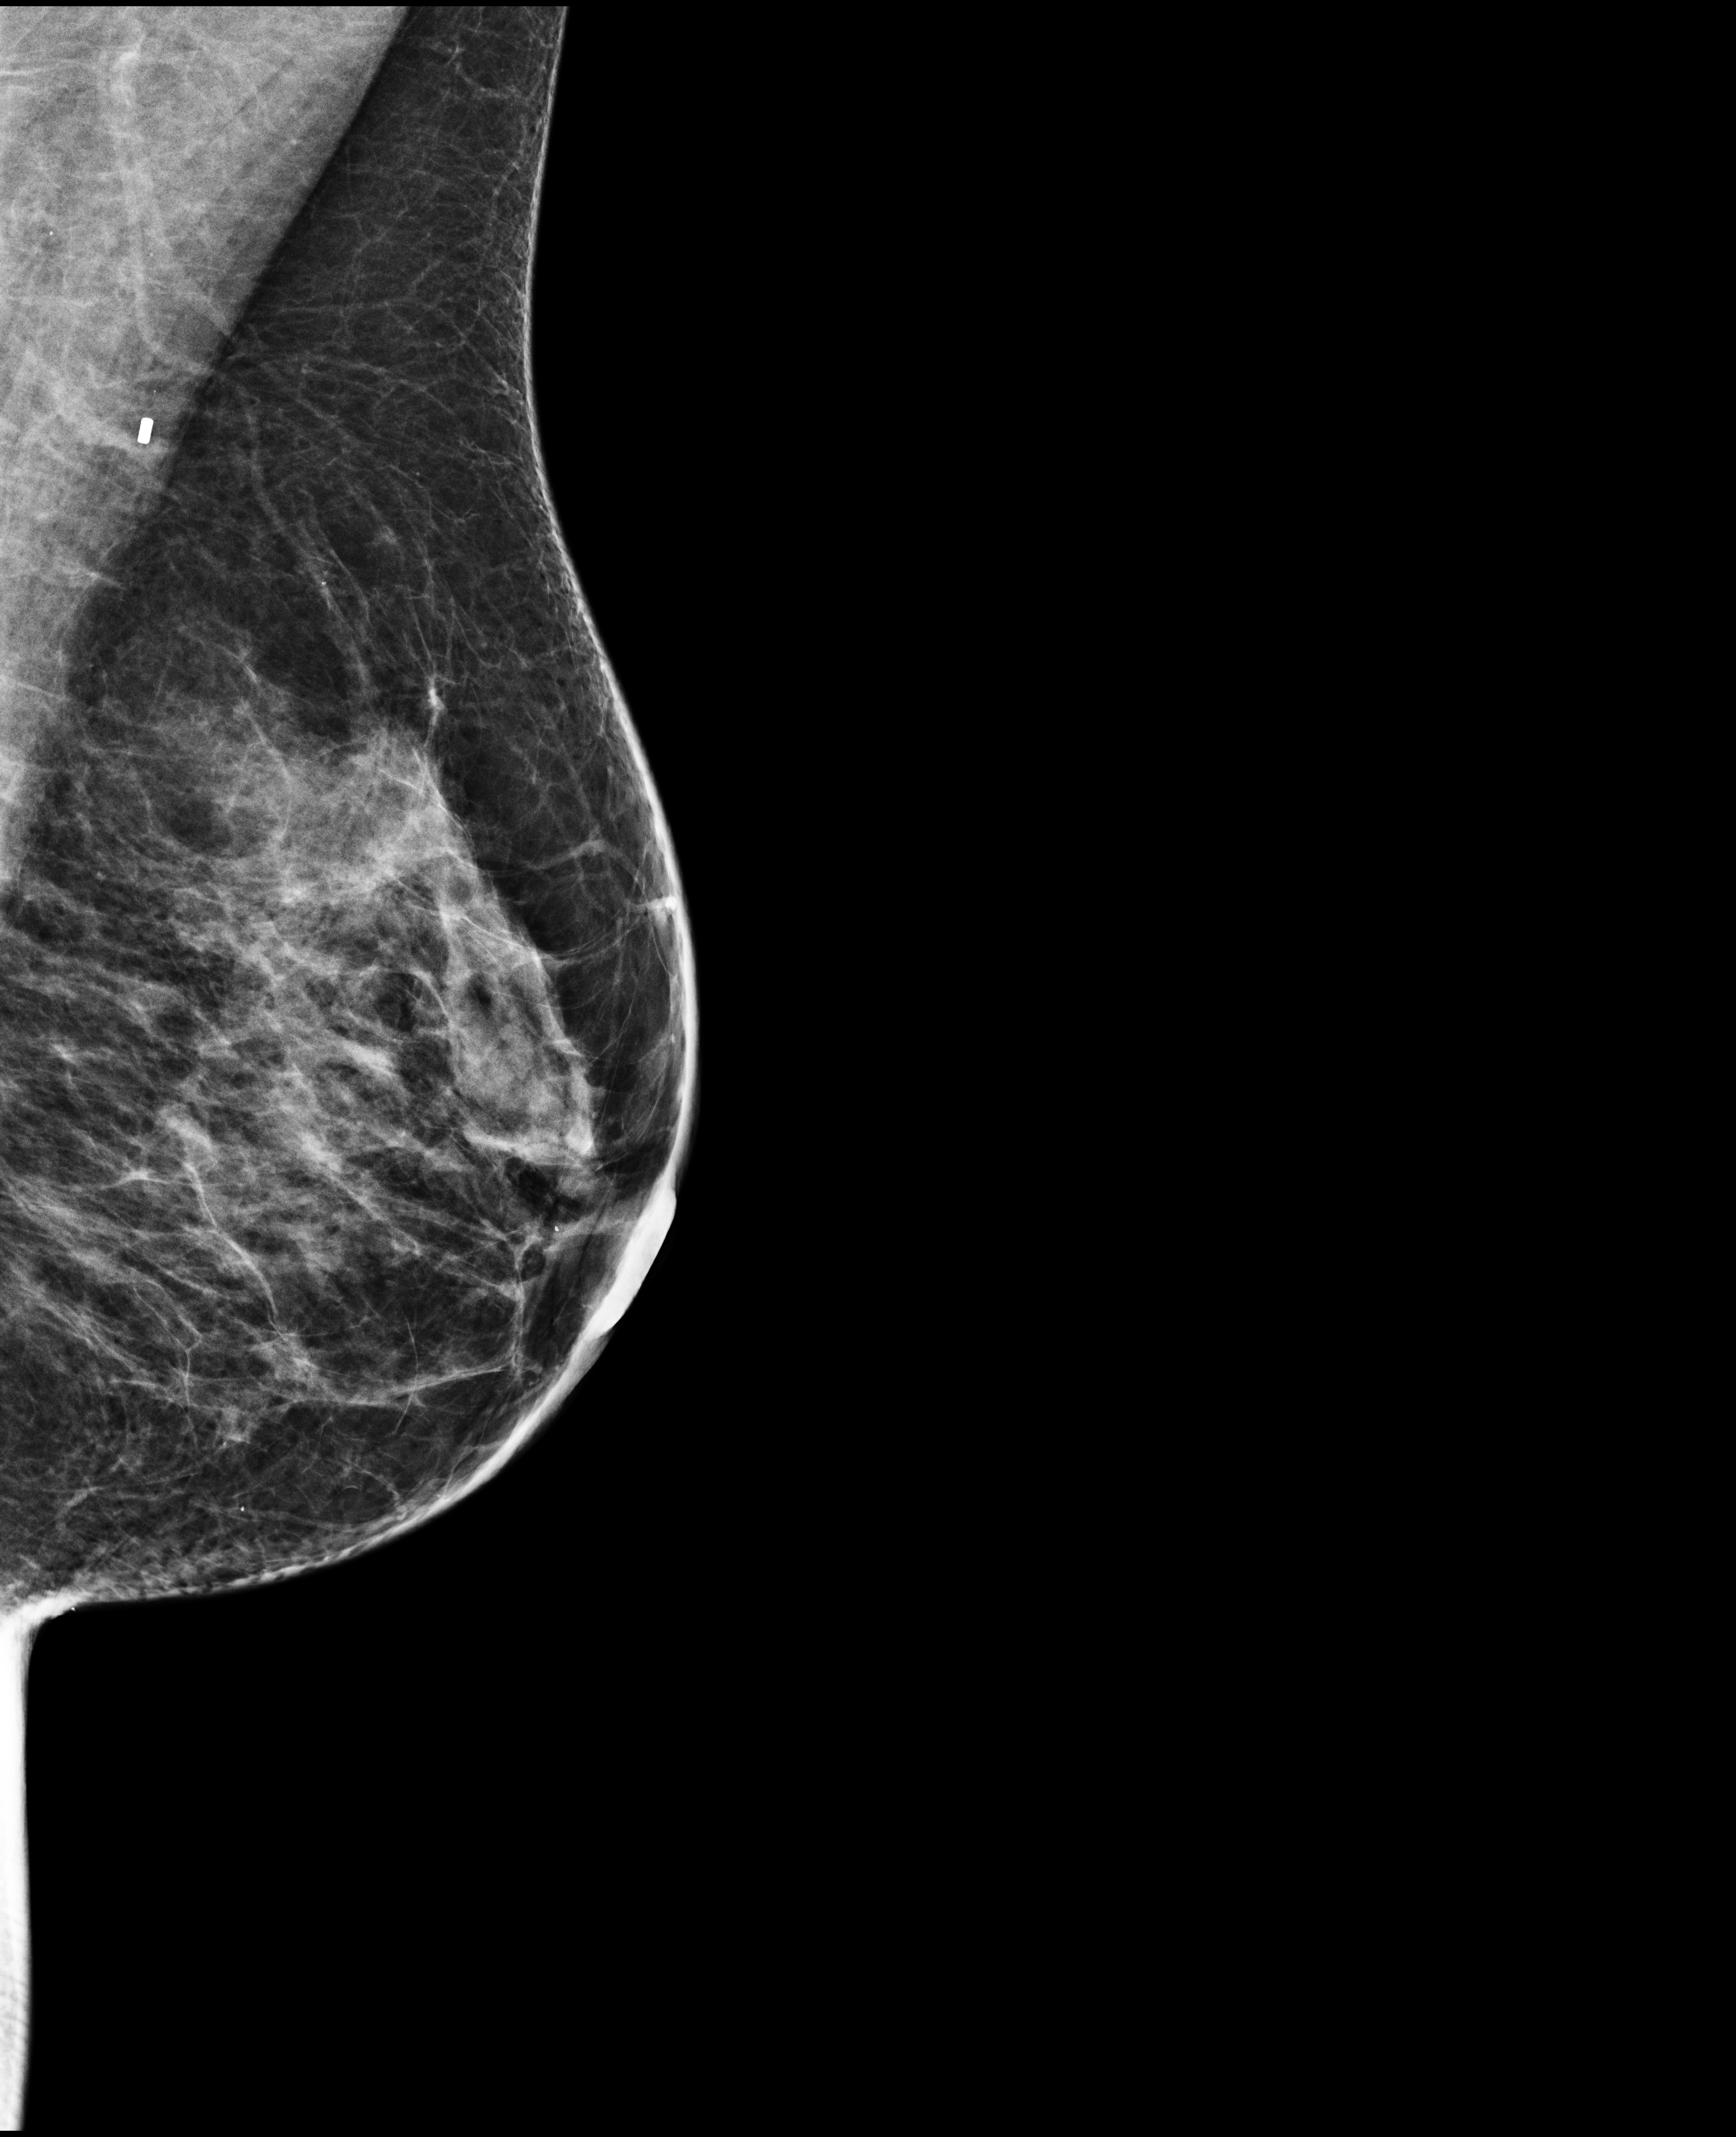
Annual screening mammography examination; compressed breast thickness 52 mm; system: Selenia Dimensions. Patient aged 47 years (female).
Image type: full-field digital mammogram. Breast: left. Projection: medio-lateral oblique projection.